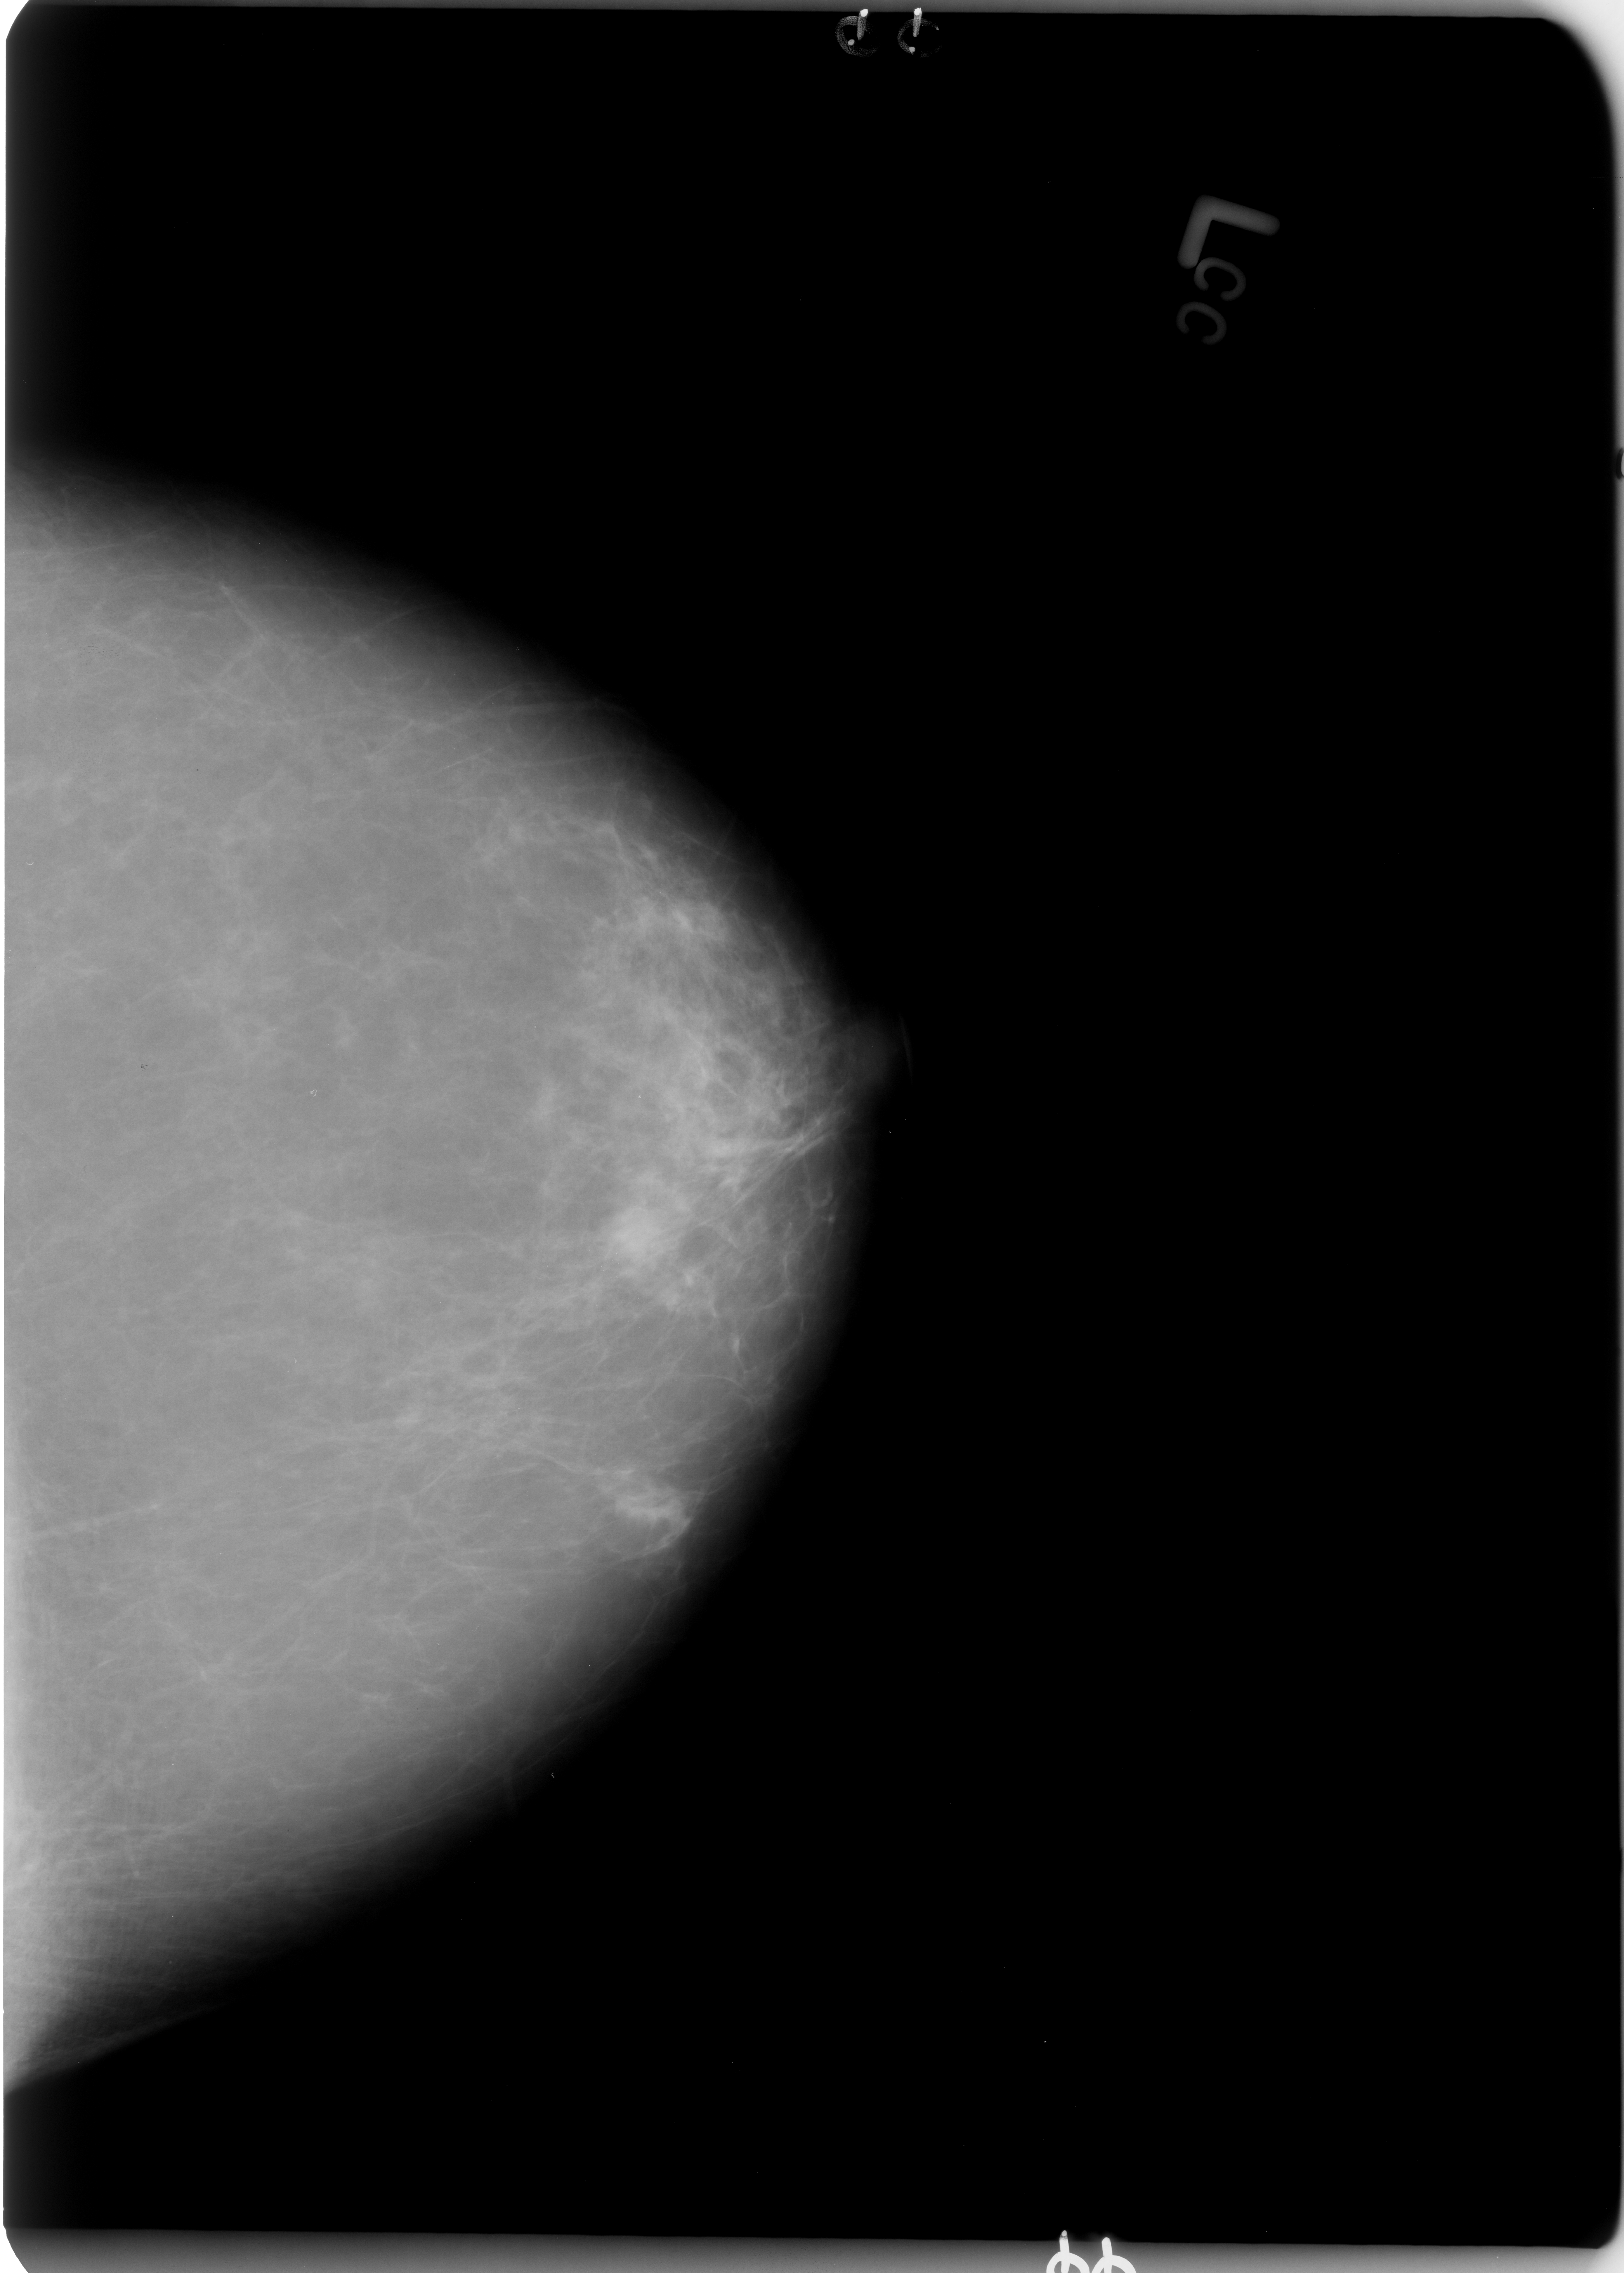
Mammogram (digitized film); left breast; CC view; breast composition: scattered fibroglandular densities (BI-RADS density category 2 of 4); 1624 × 2273 image matrix.
Expert-marked regions of interest on this image (one box per marked abnormality):
- mass, shape round, margins ill defined; BI-RADS assessment category 3; subtlety rating 4 on a 1 (subtle) to 5 (obvious) scale; pathology result (as recorded, not read from the image): benign: bounding box <591,1190,684,1284> (left, top, right, bottom; pixels)